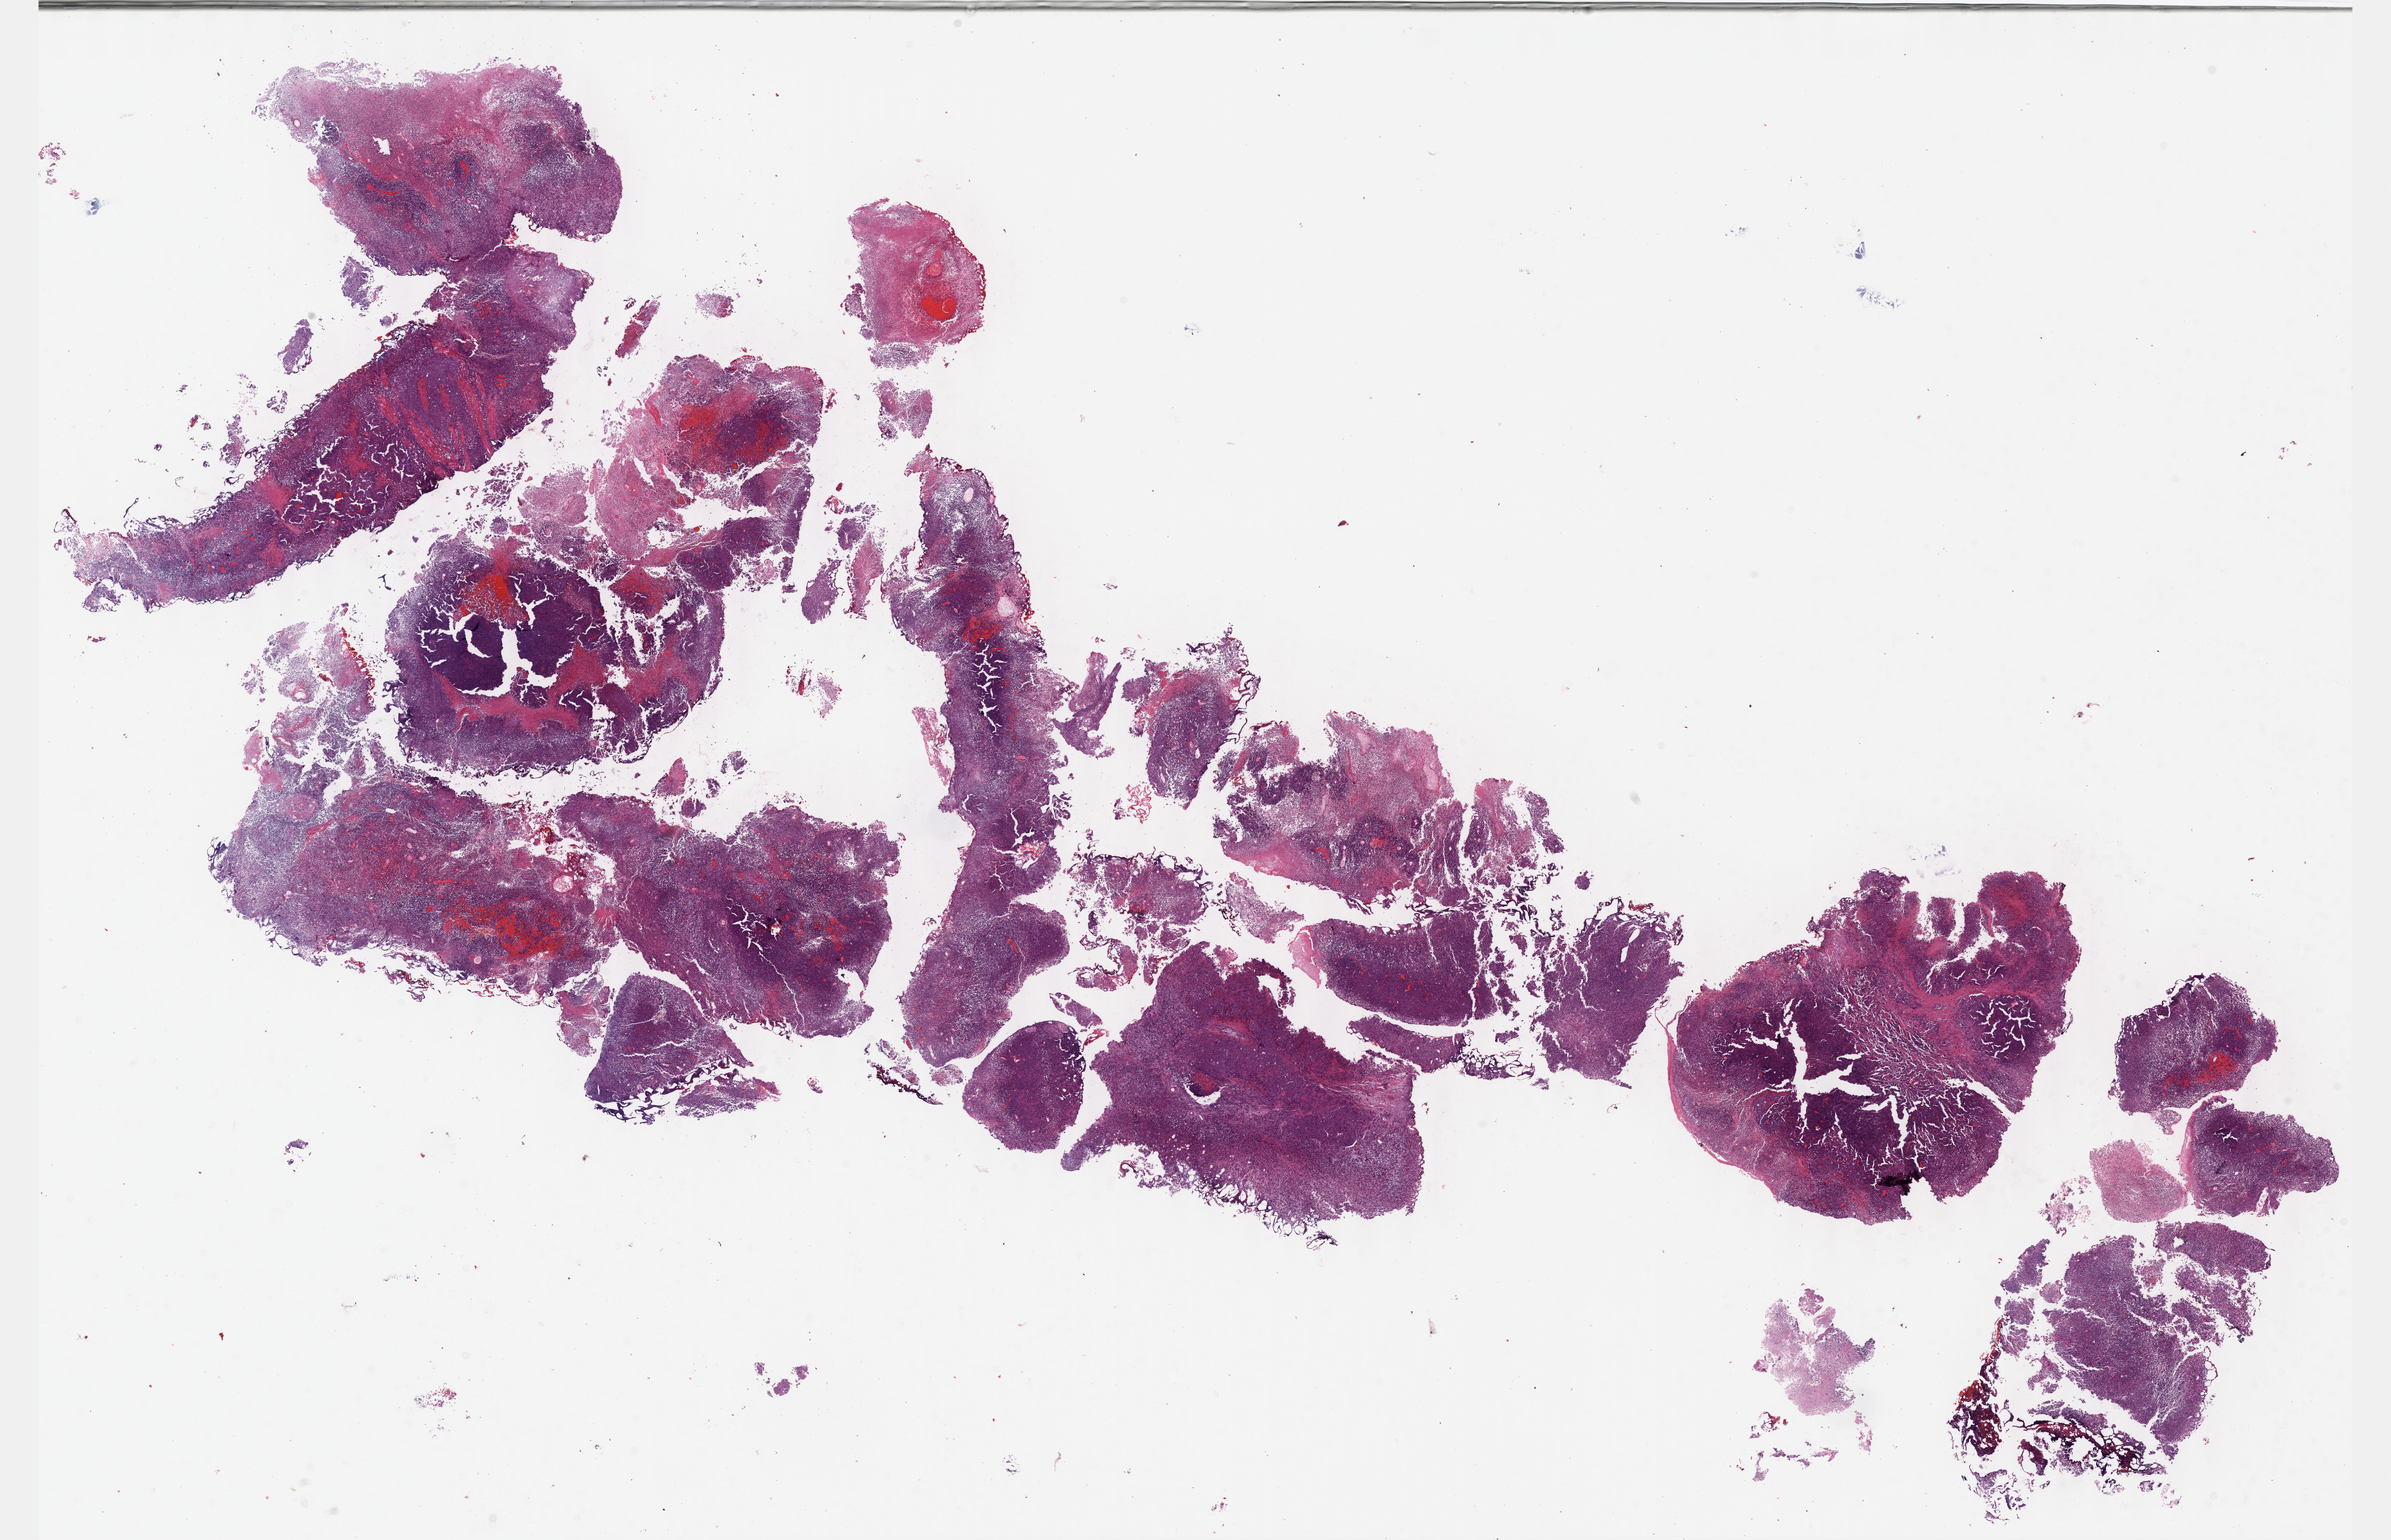
H&E whole-slide image, whole scanned area (about 31.2 x 20.1 mm, from a 40x scan) shown as a low-resolution overview. FFPE section. Primary tumour sample from the bladder. Patient: male, age at initial diagnosis 49 years. Histologic grade: high grade.
* AJCC pathologic stage: III
* TNM: T3b NX MX
* histologic diagnosis: Transitional cell carcinoma (lateral wall of bladder)